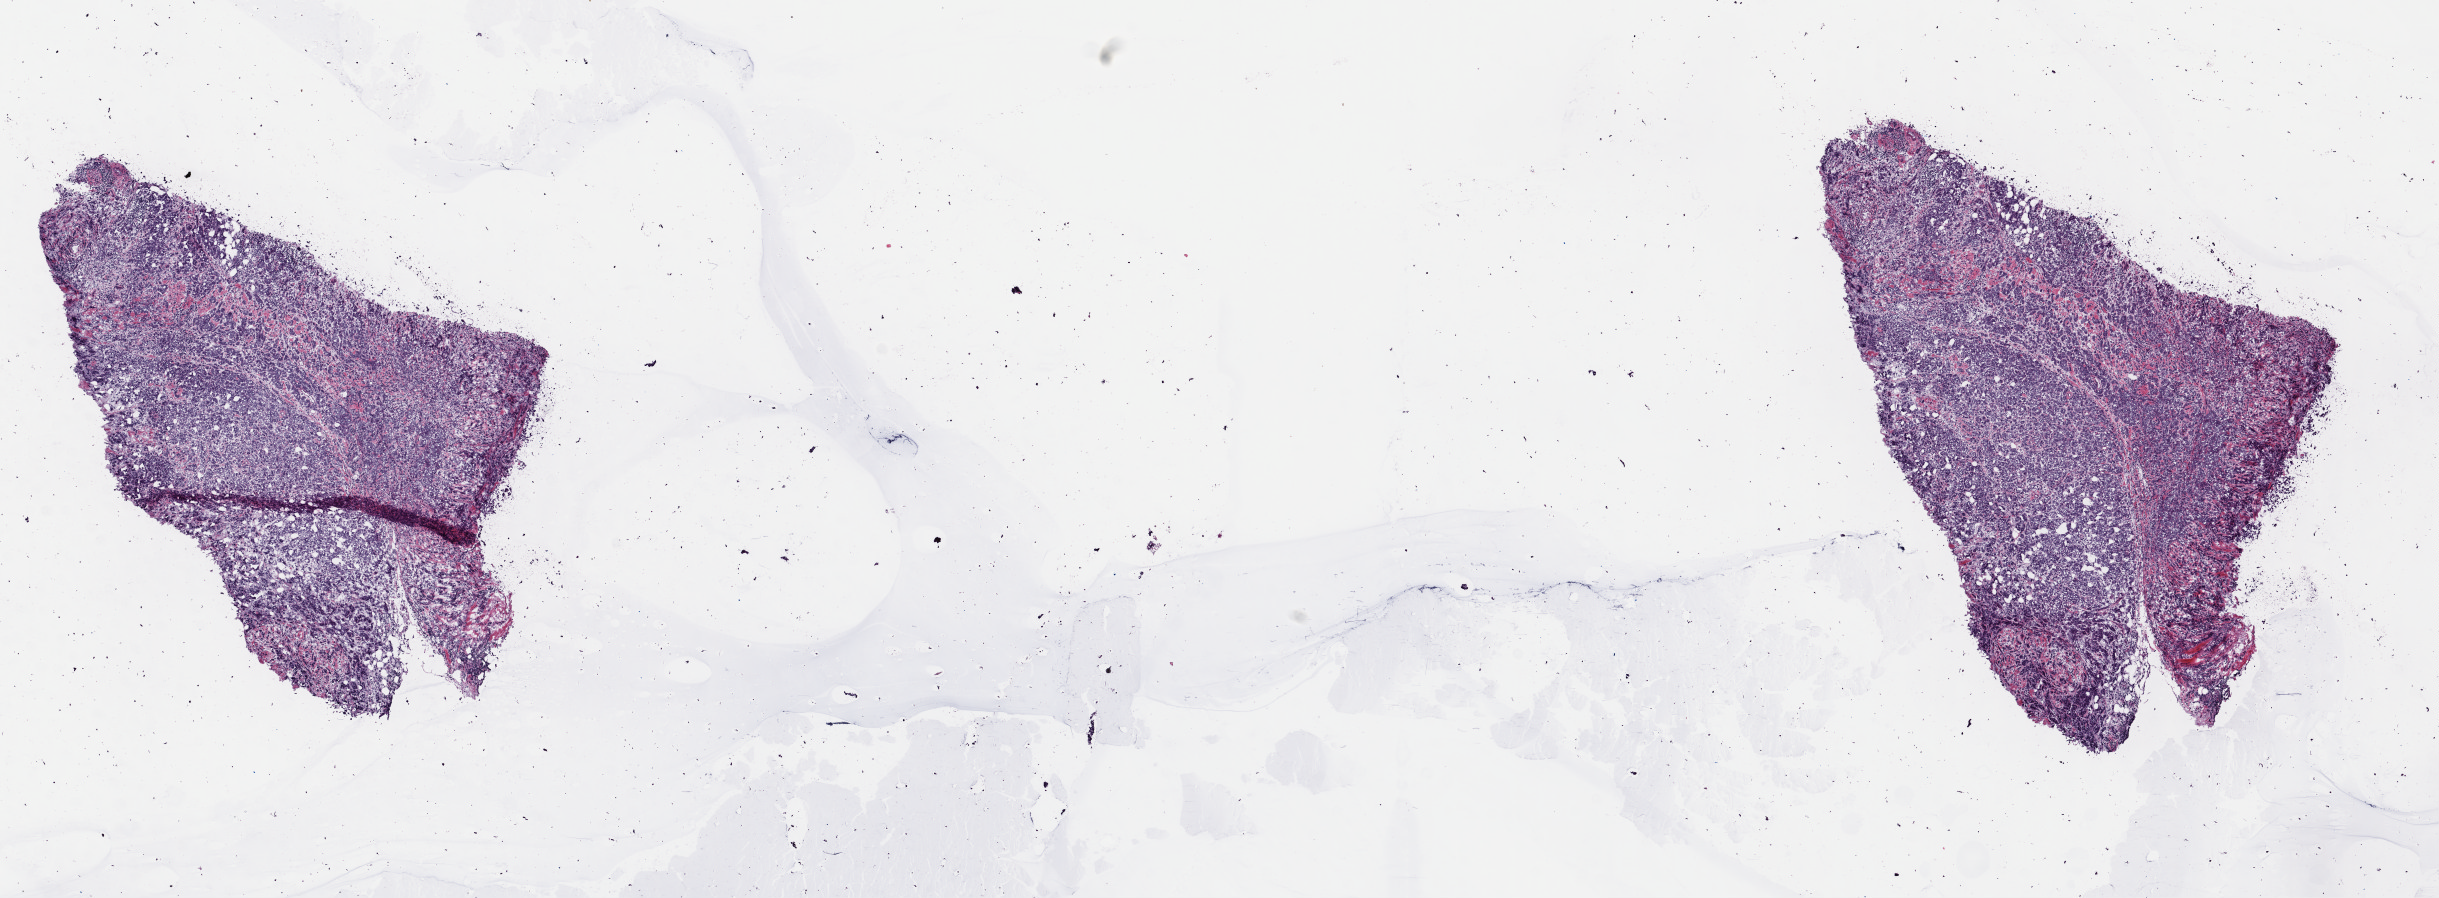
H&E whole-slide image — low-resolution overview of the scanned area, about 19.2 x 7.1 mm (slide scanned at 40x). Frozen section from the top of the tissue portion. Sample: primary tumour, breast. Patient: female, age at initial diagnosis 81 years. Composition of this section per pathologist review: tumour cells 100%, tumour nuclei 93%, normal cells 0%, stromal cells 0%, necrosis 0%. Infiltration values recorded for this section: lymphocyte infiltration 0%, monocyte infiltration 0%, neutrophil infiltration 0%.
• TNM: T2 N3a MX
• AJCC pathologic stage: IIIC (7th edition)
• diagnosis: Infiltrating duct carcinoma, NOS